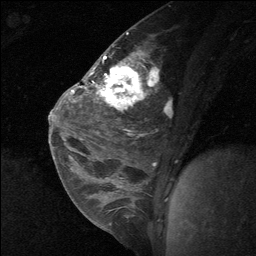
Breast MRI (dynamic contrast-enhanced), one sagittal slice; slice 37 of 64 in the series (ordered by position); dynamic contrast-enhanced study with each time point stored as its own series, time point 2 of 3 at this slice position (early post-contrast, ordered by acquisition time); 1.5 T; TE 4.8 ms, TR 27 ms; 2 mm slice thickness; 256 × 256 image matrix, field of view 180 × 180 mm. Patient: female, 26 years. From the clinical record (not read from this slice): setting: breast cancer imaged before/during neoadjuvant chemotherapy; receptor status: HR-positive, HER2-negative.
Outlined on this slice (semi-automatically segmented with operator editing):
- analysis volume of interest (the breast-tissue region the enhancement analysis was run in; not a lesion): box from (x=86, y=43) to (x=142, y=138) px
- tumour enhancement mask (voxels above the 90 % enhancement threshold inside the analysis volume of interest): (x=96, y=63)–(x=137, y=108)